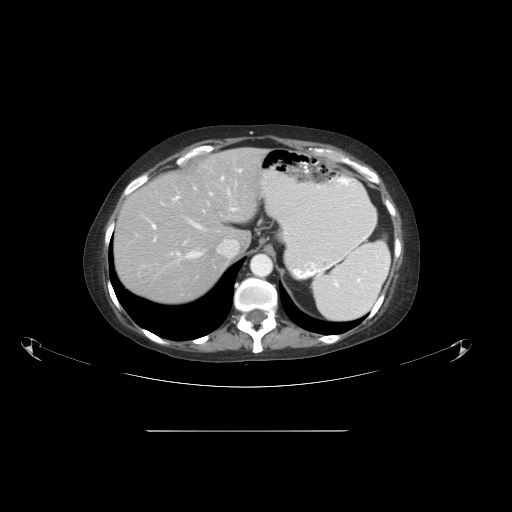
Contrast-enhanced abdominal CT, one axial slice; position 39 of 51 along the scan axis; 120 kVp; intravenous contrast given; soft-tissue window (W 400 / L 40 HU); 5 mm slice thickness; 512 × 512 image matrix, field of view 475 × 475 mm. Female patient, age 48 years. Case-level facts recorded for this patient, not image findings: diagnosis: colorectal cancer liver metastases, imaged before liver resection; multiple liver metastases: yes; largest metastasis: 1 cm; chemotherapy before resection: no.
Outlined on this slice (expert manual segmentation):
- hepatic veins: bounding box <186,189,238,258> (left, top, right, bottom; pixels)
- liver: <115,149,266,304>
- planned liver remnant (the part of the liver to remain after resection): <115,172,229,304>
- portal vein (with intrahepatic branches): <152,169,242,256>